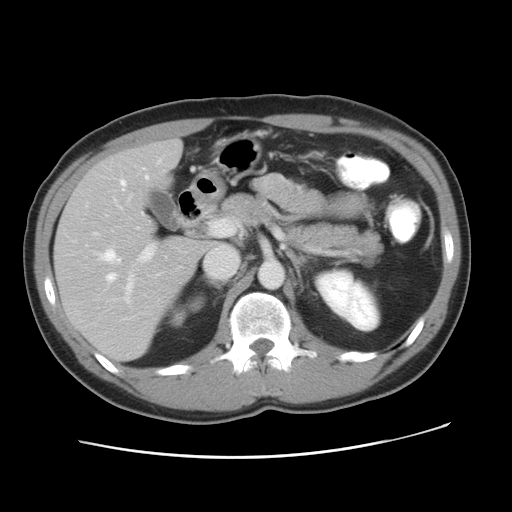
Contrast-enhanced abdominal CT, one axial slice. Intravenous contrast given. Soft-tissue window (W 400 / L 40 HU). 5 mm slice thickness. 512 × 512 image matrix, field of view 363 × 363 mm. Male patient, age 41 years. From the clinical record (not read from this slice): diagnosis: colorectal cancer liver metastases, imaged before liver resection; multiple liver metastases: yes; largest metastasis: 0.7 cm.
Outlined on this slice (outlined manually by an expert reader):
- hepatic veins: bounding box [x1, y1, x2, y2] px = [92, 158, 238, 284]
- liver: [55, 141, 210, 361]
- planned liver remnant (the part of the liver to remain after resection): [106, 141, 182, 196]
- portal vein (with intrahepatic branches): [115, 200, 154, 301]